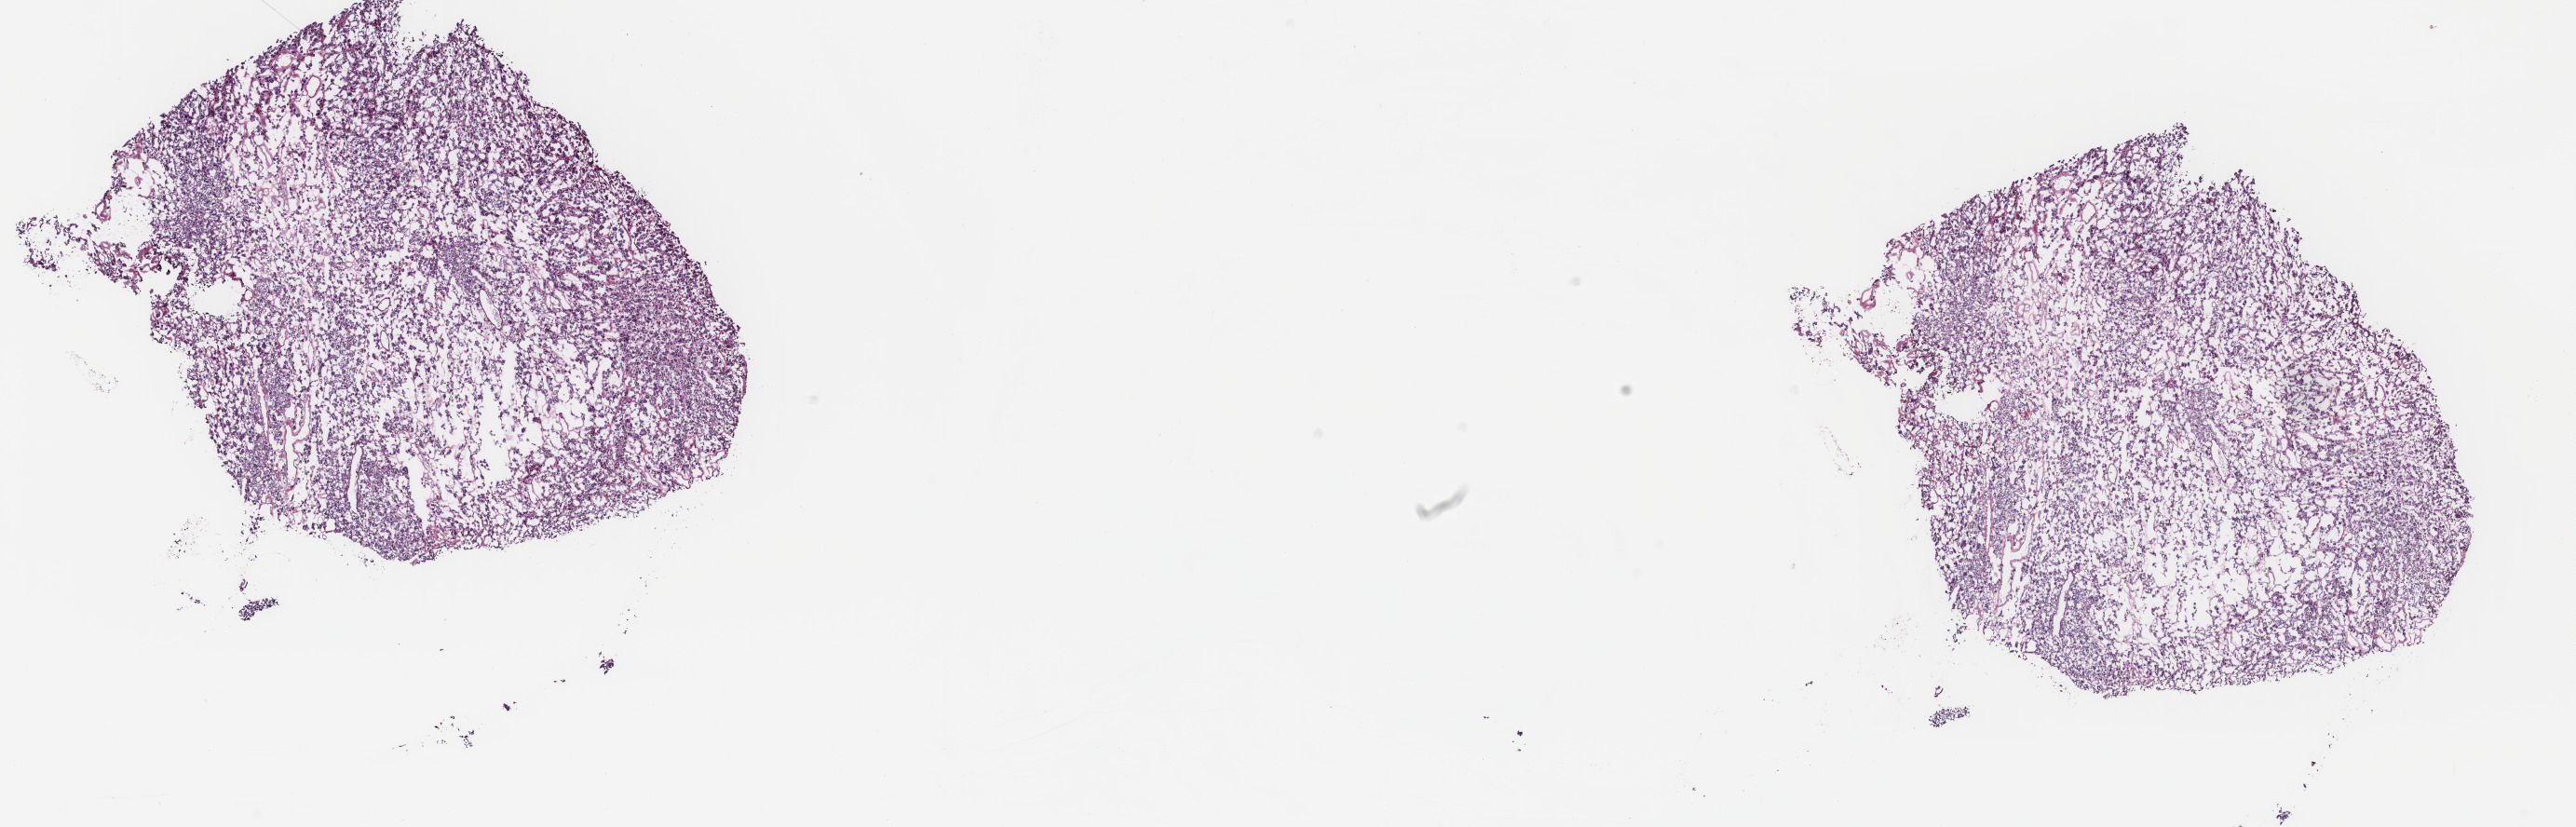
Hematoxylin and eosin (H&E) stained whole-slide image — low-resolution overview of the scanned area, about 22.0 x 7.0 mm (slide scanned at 40x); frozen section from the top of the tissue portion; thyroid, primary tumour sample. Patient: female, age at initial diagnosis 61 years. Slide review estimates, as recorded: tumour cells 100%, tumour nuclei 85%, normal cells 0%, stromal cells 0%, necrosis 0%. Inflammatory infiltration, as recorded: lymphocyte infiltration 1%, monocyte infiltration 0%, neutrophil infiltration 0%.
* AJCC pathologic stage: I
* histologic diagnosis: Papillary adenocarcinoma, NOS